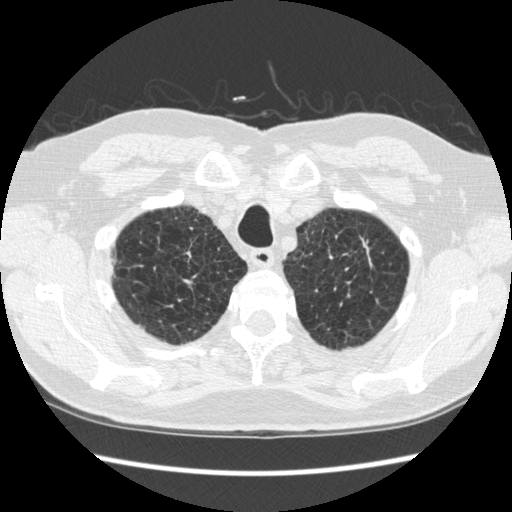
Chest CT (low-dose screening protocol), one axial image. Second annual screen. Lung window (W 1500 / L -600 HU). 1.25 mm slice thickness. Standard (soft-tissue) reconstruction kernel (STANDARD). 120 kVp. Male participant, aged 70 years at enrolment. Former smoker at enrolment.
Lesion marked by an expert reader, box from (x=329, y=222) to (x=390, y=290) px. The screening reader recorded 5 non-calcified nodules or masses ≥4 mm on this exam (right lower lobe, right lower lobe, right lower lobe, left upper lobe, left lower lobe); which of them this box marks is not recorded. Lung cancer was diagnosed 479 days after this screen: squamous cell carcinoma, NOS, left upper lobe, moderately differentiated (G2), stage IA (AJCC 6th edition), 18 mm at pathology.